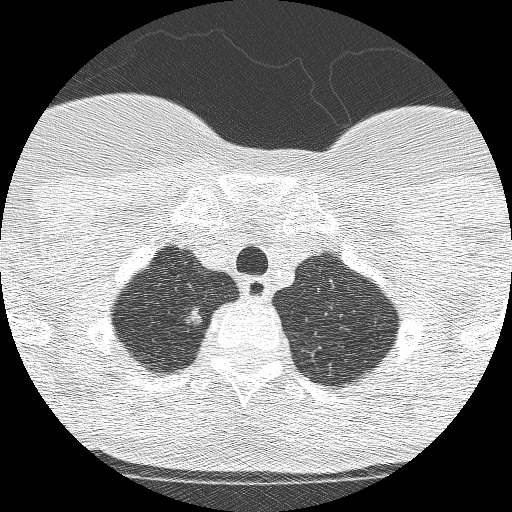
Chest CT (low-dose screening protocol), one axial image; second annual screen; lung window (W 1500 / L -600 HU); 1.25 mm slice thickness; 512 × 512 image matrix, field of view 257 × 257 mm. Female participant, aged 61 years at enrolment.
Expert-annotated lung lesion, bounding box [x1, y1, x2, y2] px = [164, 298, 214, 338]. Reader record for this screening exam (exam-level; its link to the box is not recorded): non-calcified nodule or mass ≥4 mm, right upper lobe, 11 × 8 mm, poorly defined margins, mixed attenuation, pre-existing on the prior screen: yes; interval growth: yes. Official screen result: positive, change unspecified: nodule(s) >= 4 mm or enlarging nodule(s), mass(es), or other non-specific abnormalities suspicious for lung cancer. Later outcome: lung cancer diagnosed 28 days after this screen — adenocarcinoma, NOS, right upper lobe, poorly differentiated (G3), 12 mm at pathology.